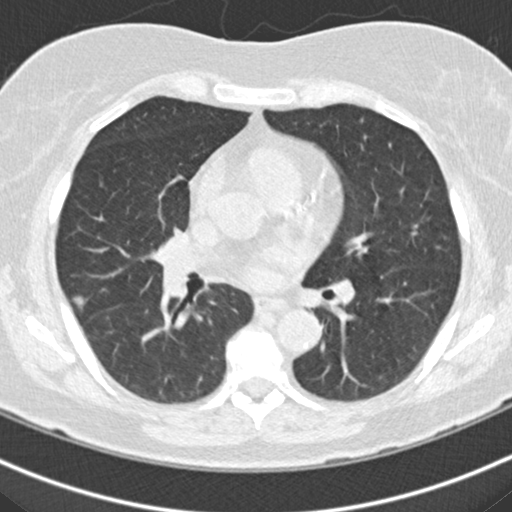
Low-dose screening chest CT, one axial slice; position 101 of 160 along the scan axis; 120 kVp; lung window (W 1500 / L -600 HU); 2 mm slice thickness; 512 × 512 image matrix.
Outlined on this slice (expert manual segmentation):
- lesion 2 (tumor, middle lobe of right lung): bounding box (x1, y1, x2, y2) in pixels: (74, 296, 85, 309)